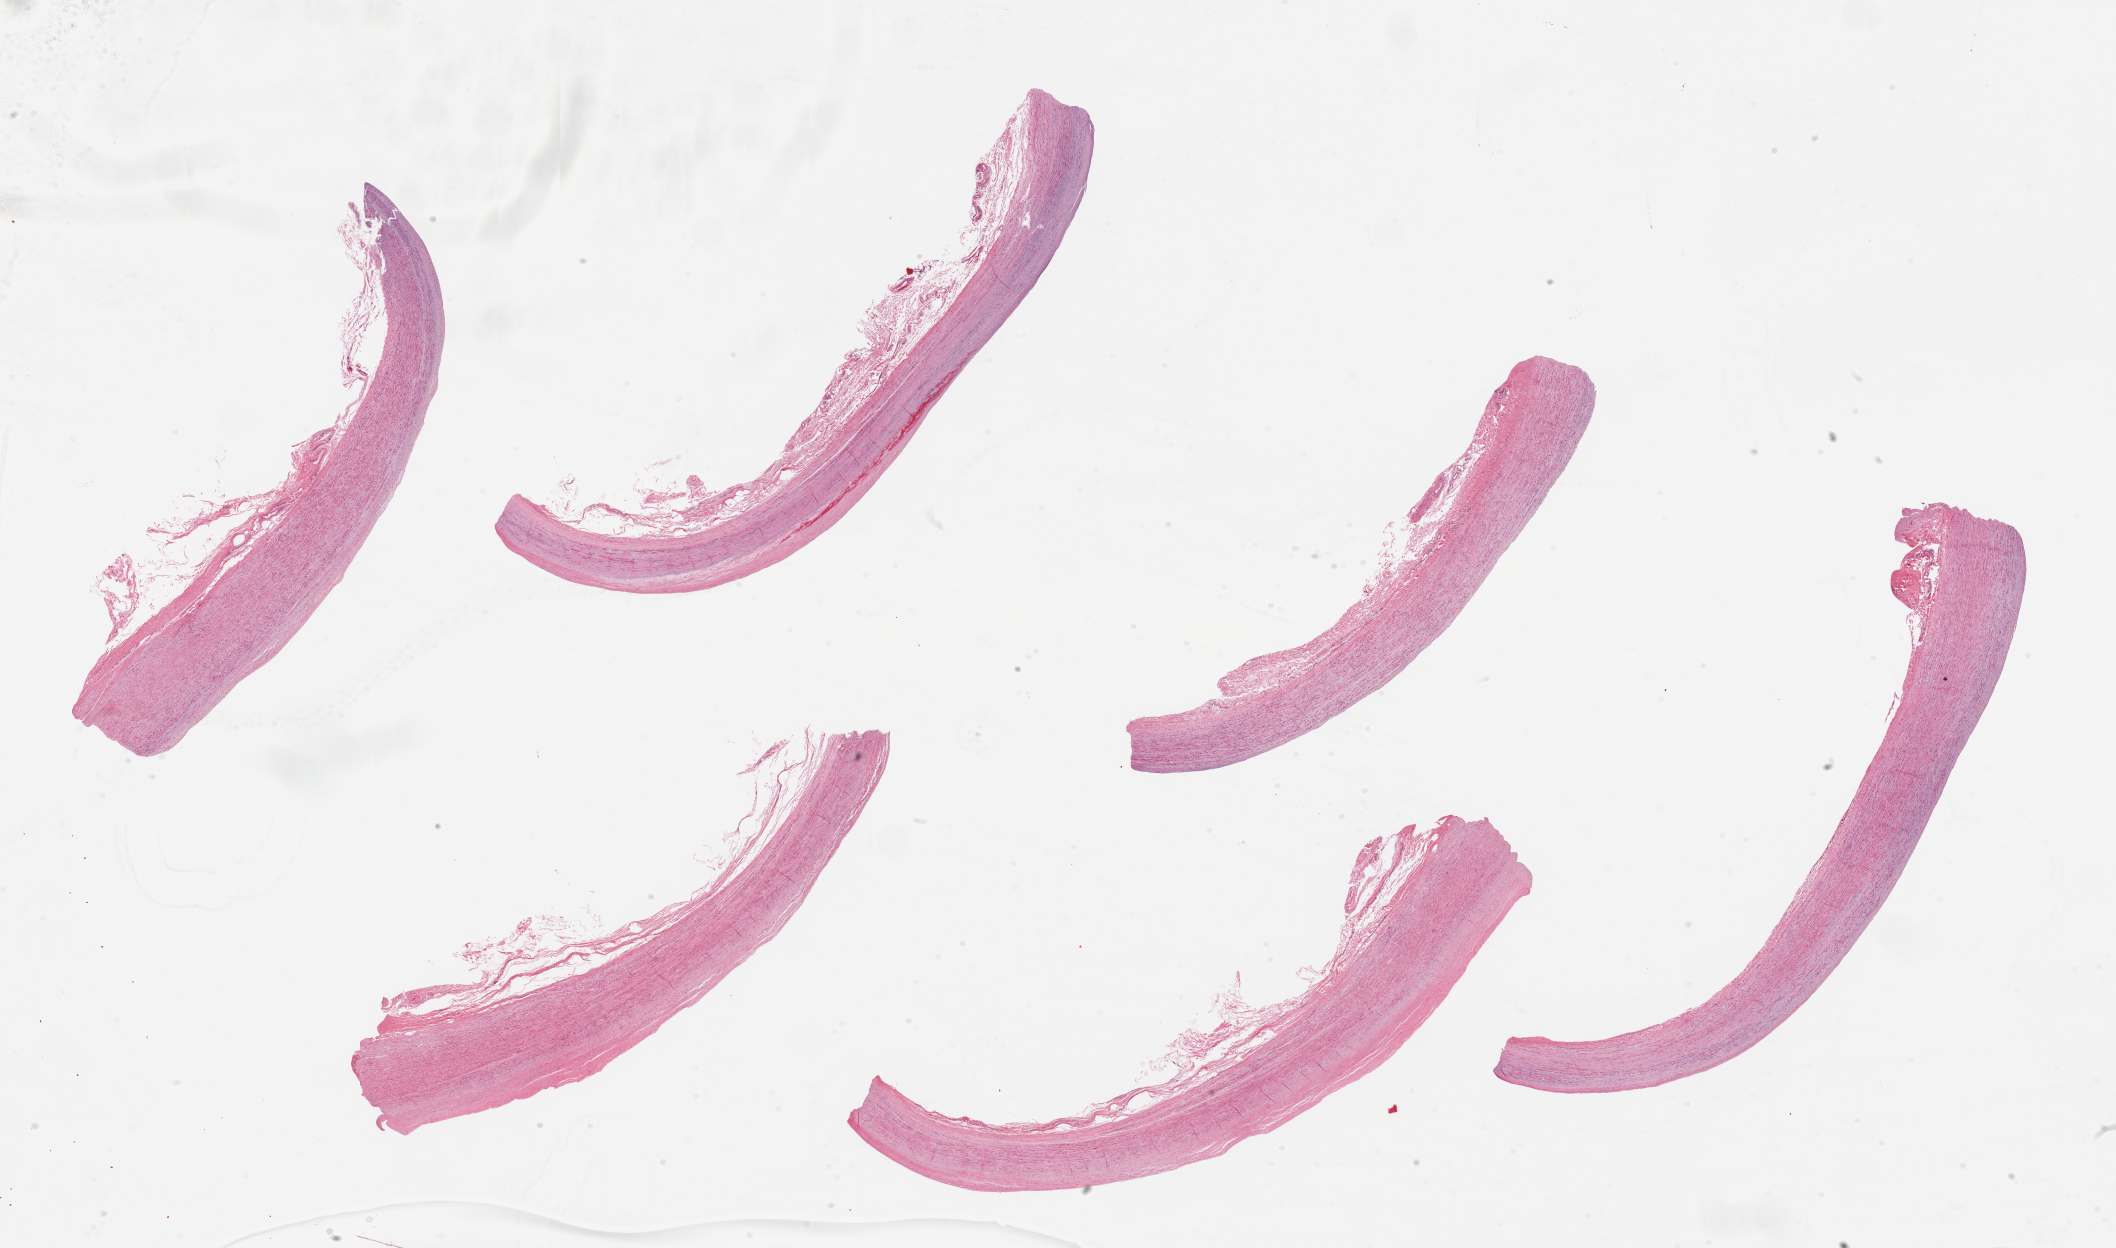
Digitized hematoxylin and eosin (H&E)-stained section — whole scanned area (about 33.5 x 19.7 mm, slide scanned at 20x) shown as a low-resolution overview; PAXgene-fixed paraffin-embedded (PFPE) section; target tissue: aorta; donor tissue sample.
• reviewer comment on this tissue sample: 6 pieces up to 10x1.5 mm; flat plaques; small intramural hemorrhage